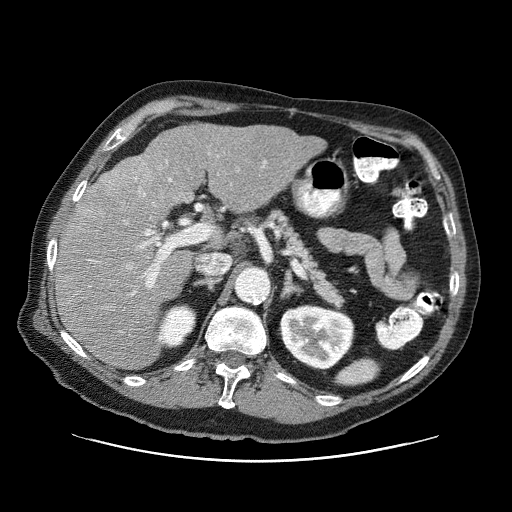
Contrast-enhanced abdominal CT (liver protocol), one axial slice; position 41 of 87 along the scan axis; reconstruction kernel STANDARD; 120 kVp; one of 3 acquisitions stored at this slice position; soft-tissue window (W 400 / L 40 HU); 2.5 mm slice thickness; 512 × 512 image matrix, field of view 400 × 400 mm. From the clinical record (not read from this slice): diagnosis: hepatocellular carcinoma (patient treated with transarterial chemoembolisation; whether this scan precedes or follows treatment is not stated here); TNM stage (as recorded): Stage-IIIA; Child-Pugh class: A; tumour nodularity: multinodular; tumour size: 6 cm.
Annotated regions visible in this slice (semi-automatic segmentation, software-assisted and operator-edited):
- liver parenchyma outside the tumour (the mass and vessels are separate outlines, so this box may not span the whole liver): box from (x=56, y=124) to (x=326, y=368) px
- mass: (x=97, y=156)–(x=151, y=204)
- liver vessels: (x=93, y=160)–(x=266, y=295)